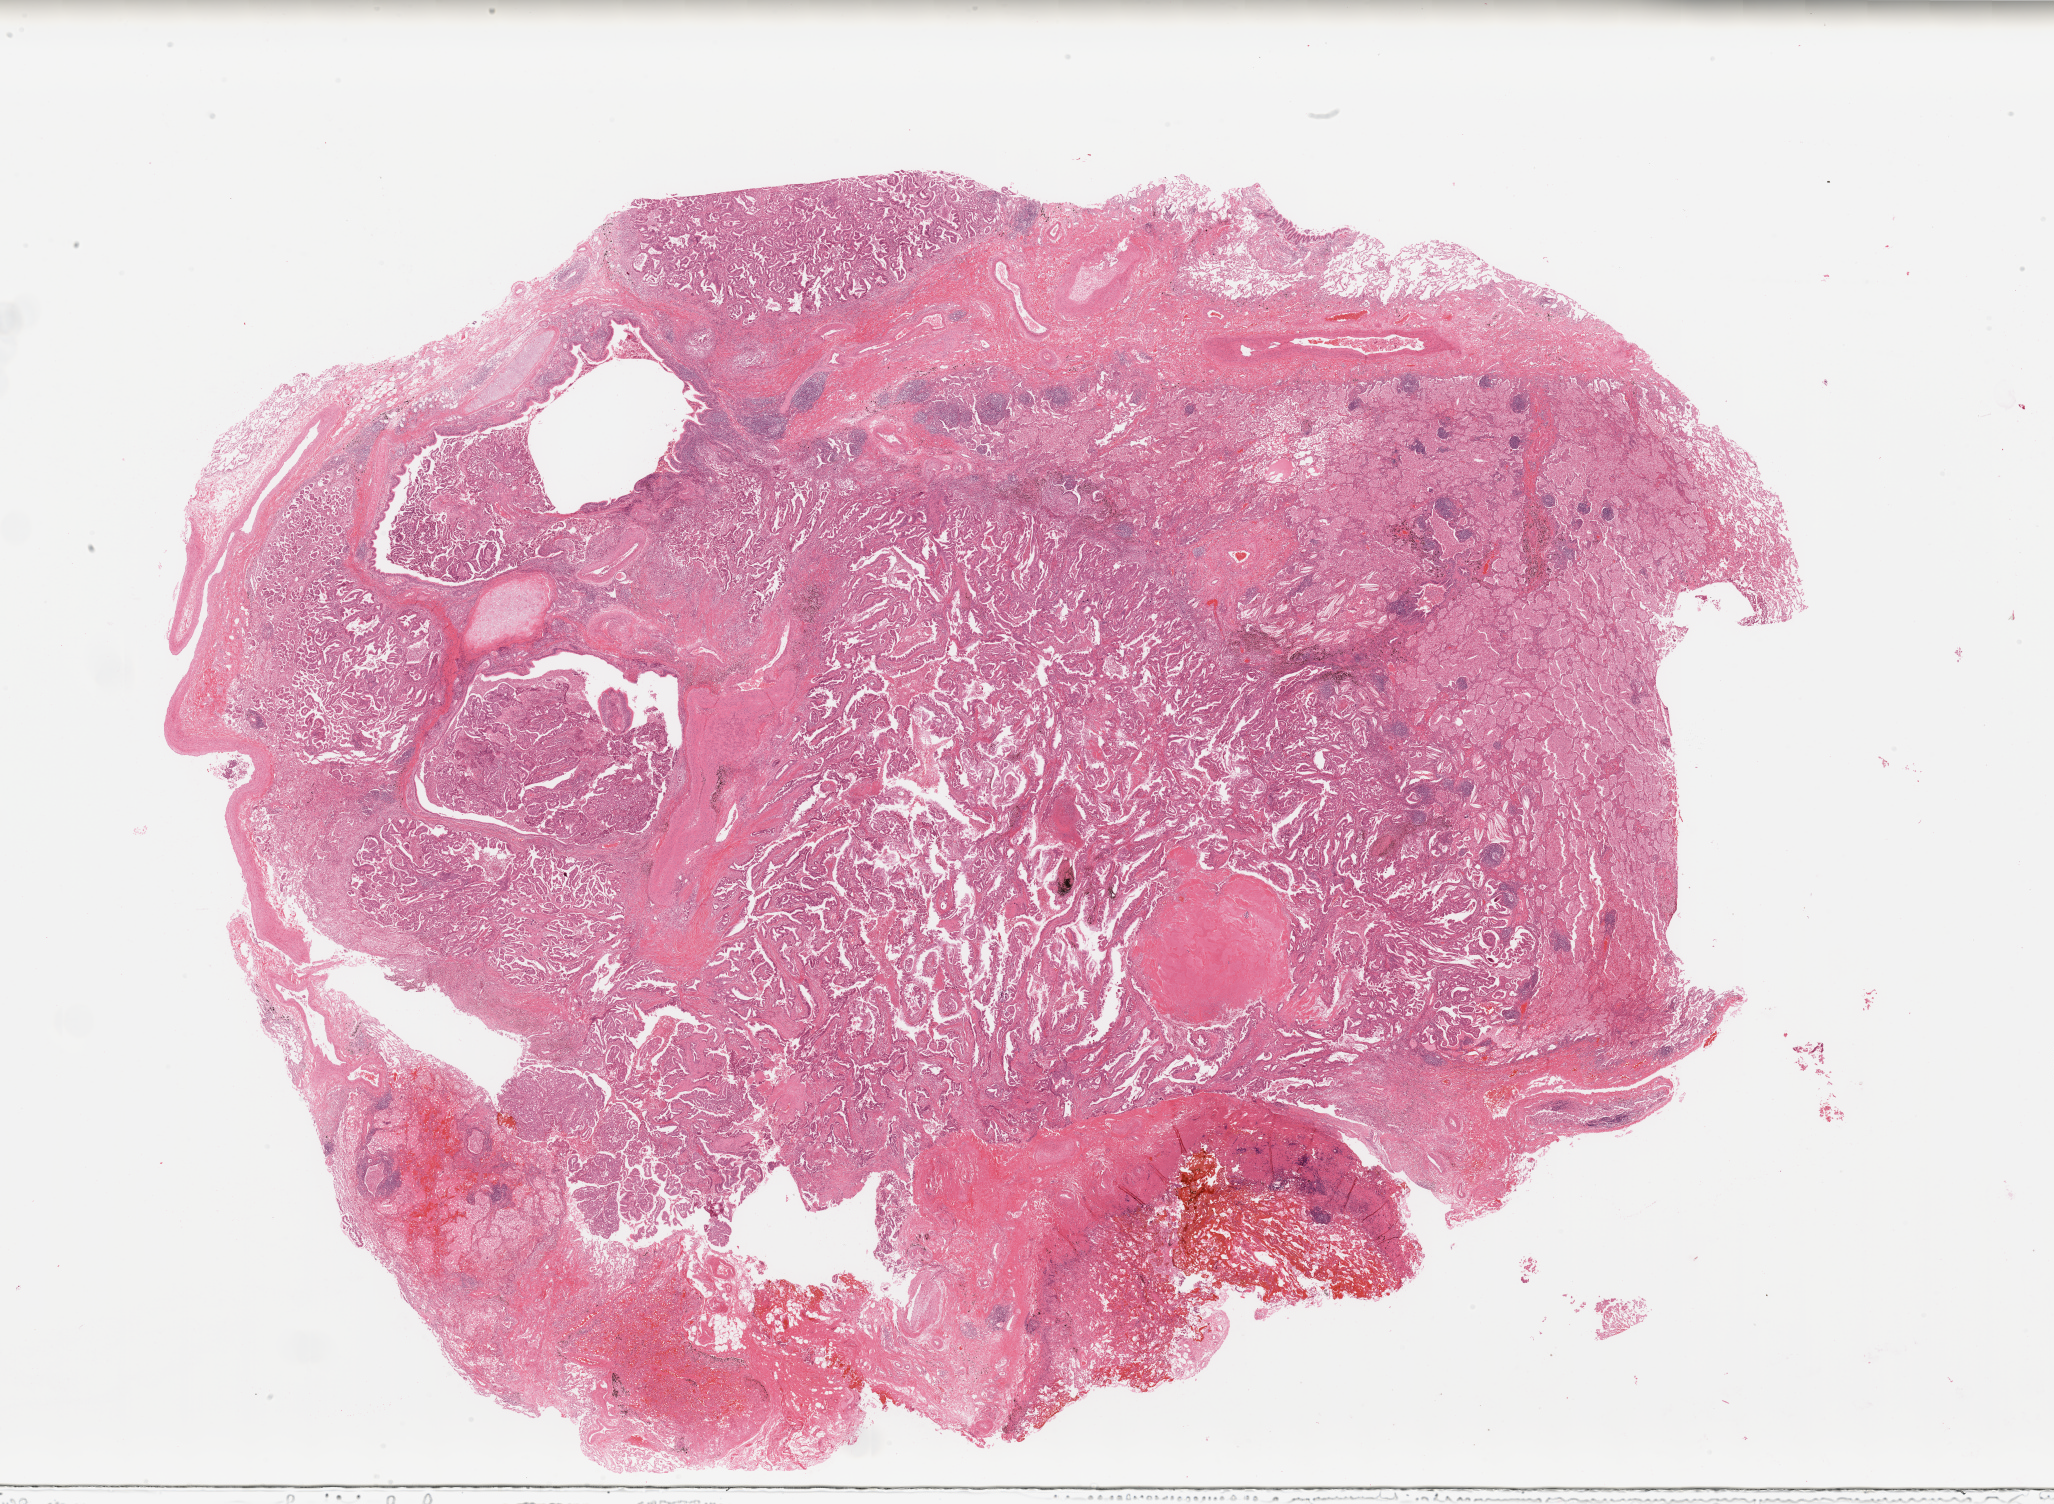
Digitized H&E-stained tissue section (whole slide) — a low-resolution overview of the entire scanned area, about 32.5 x 23.8 mm (slide scanned at 20x), tumour tissue sample, lung. 67-year-old male patient. Histologic grade: G2 (moderately differentiated).
AJCC pathologic stage: IIIA. Histologic diagnosis: Adenocarcinoma, NOS.